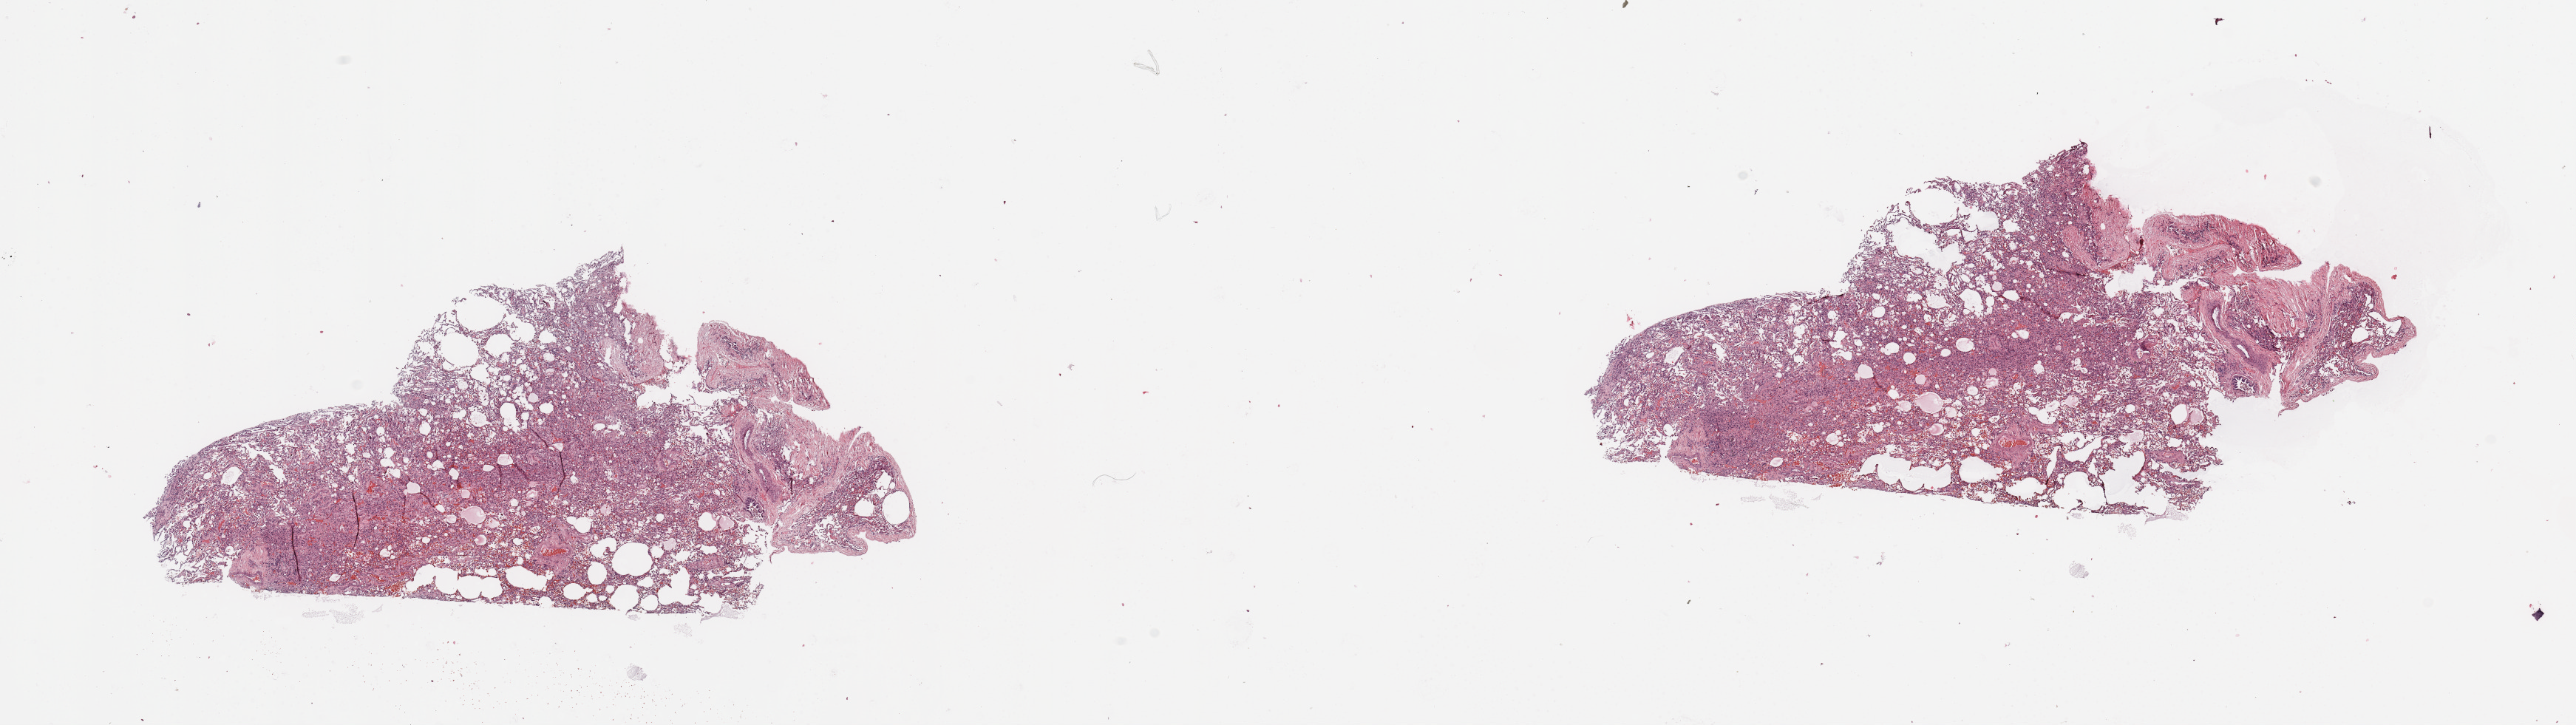
Digitized H&E tissue section (whole slide), low-resolution overview of the scanned area, about 27.6 x 7.8 mm (acquisition: 20x scan), normal (non-tumour) tissue sample, lung. Male, 57 y/o.
This section: normal (non-tumour) tissue from the same patient. Patient diagnosis: Squamous cell carcinoma, NOS.